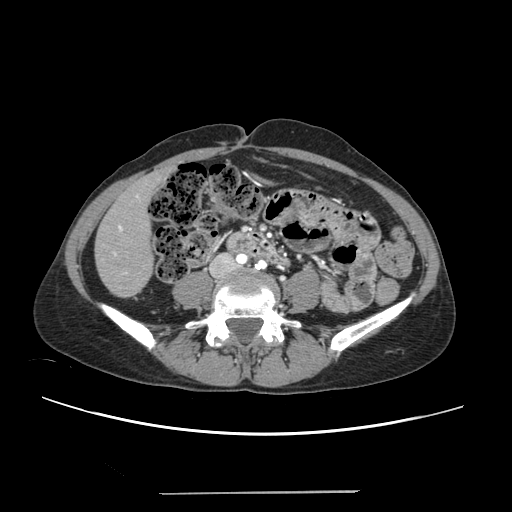
Contrast-enhanced abdominal CT, one axial slice. Slice 44 of 240 in the series (ordered by position). 120 kVp. Intravenous contrast given. Soft-tissue window (W 400 / L 40 HU). 512 × 512 image matrix, field of view 371 × 371 mm. Female patient, age 60 years. From the clinical record (not read from this slice): diagnosis: colorectal cancer liver metastases, imaged before liver resection; multiple liver metastases: no; largest metastasis: 1.5 cm; disease in both lobes: no.
Annotated regions visible in this slice (manually delineated by an expert):
- liver: bounding box (x1, y1, x2, y2) in pixels: (96, 171, 167, 296)
- planned liver remnant (the part of the liver to remain after resection): (96, 172, 166, 296)
- portal vein (with intrahepatic branches): (113, 195, 138, 274)